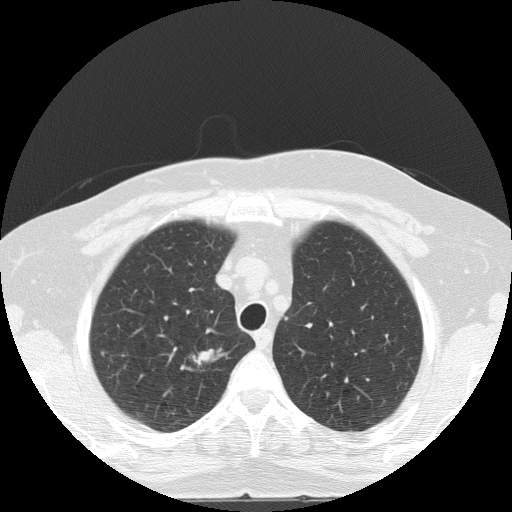
Axial slice from a low-dose chest CT screening exam. Baseline annual screen. Lung window (W 1500 / L -600 HU). Lung (sharp) reconstruction kernel (FC51). Slice 26 of 133 in the series. Female, age 56 years at enrolment. Current smoker at enrolment.
Lesion marked by an expert reader, bounding box <168,333,237,390> (left, top, right, bottom; pixels). The screening reader recorded 2 non-calcified nodules or masses ≥4 mm on this exam (right upper lobe, right lower lobe); which of them this box marks is not recorded. Official screen result: positive, change unspecified: nodule(s) >= 4 mm or enlarging nodule(s), mass(es), or other non-specific abnormalities suspicious for lung cancer. Lung cancer was diagnosed 24 days after this screen: adenocarcinoma, NOS, right upper lobe, poorly differentiated (G3), stage IA (AJCC 6th edition), 20 mm at pathology.